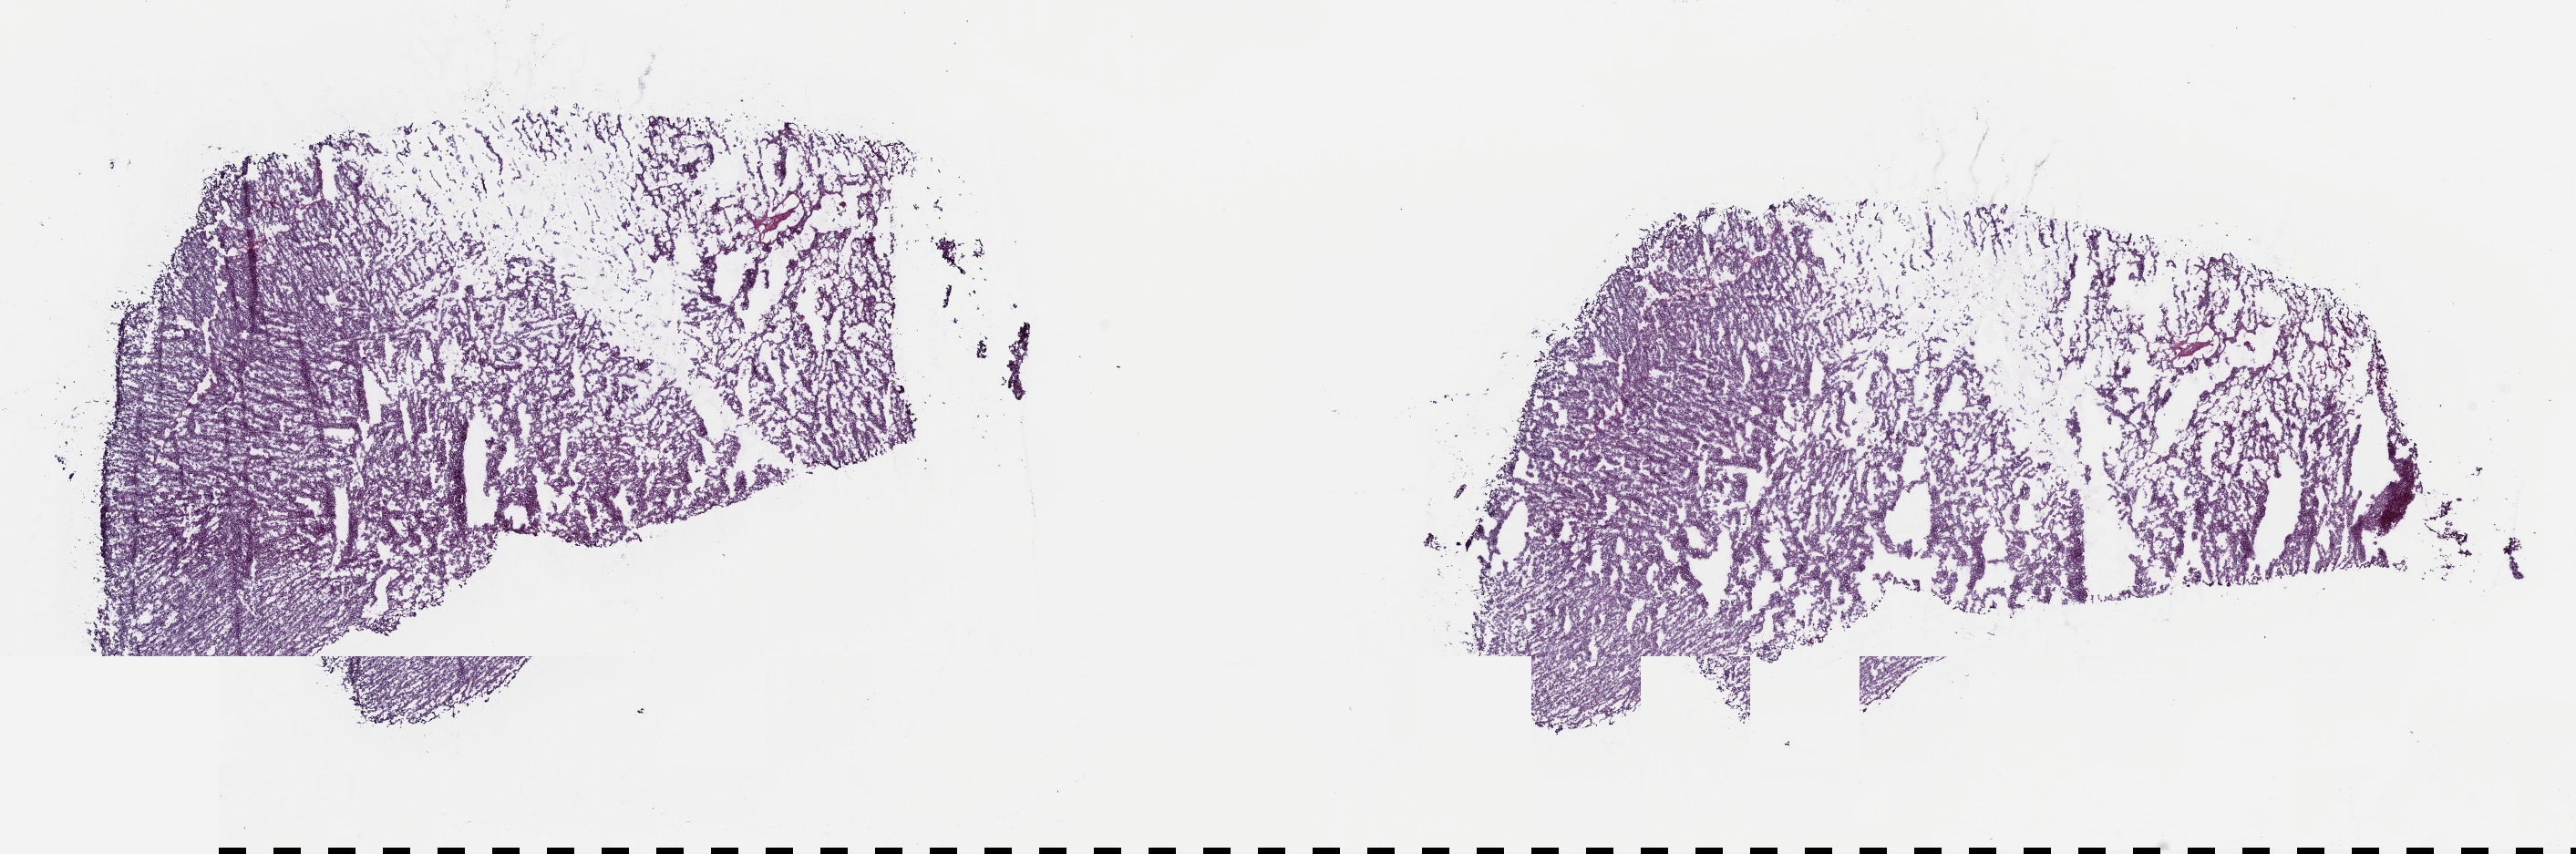
Whole-slide histology image, H&E — whole scanned area (about 22.3 x 7.4 mm) shown as a low-resolution overview; frozen section; adrenal cortex, primary tumour sample. Patient: male, age at initial diagnosis 72 years. Slide review estimates, as recorded: tumour cells 95%, tumour nuclei 100%, normal cells 0%, stromal cells 5%, necrosis 0%. Infiltration values recorded for this section: lymphocyte infiltration 0%, monocyte infiltration 0%, neutrophil infiltration 0%.
• pathologic diagnosis: Adrenal cortical carcinoma (cortex of adrenal gland)